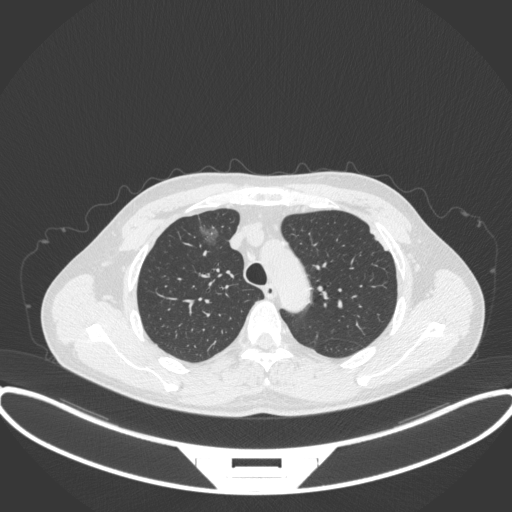
Chest CT, one axial slice; slice 276 of 395 in the series (ordered by position); 120 kVp; lung window (W 1500 / L -600 HU); 1 mm slice thickness; 512 × 512 image matrix. Patient: male, 60 years. From the clinical record (not read from this slice): clinical TNM (as recorded): T1c N0 M0.
Annotated regions visible in this slice (rectangle marked by the reading radiologist):
- lung tumour (recorded histology: adenocarcinoma): box from (x=186, y=211) to (x=224, y=258) px